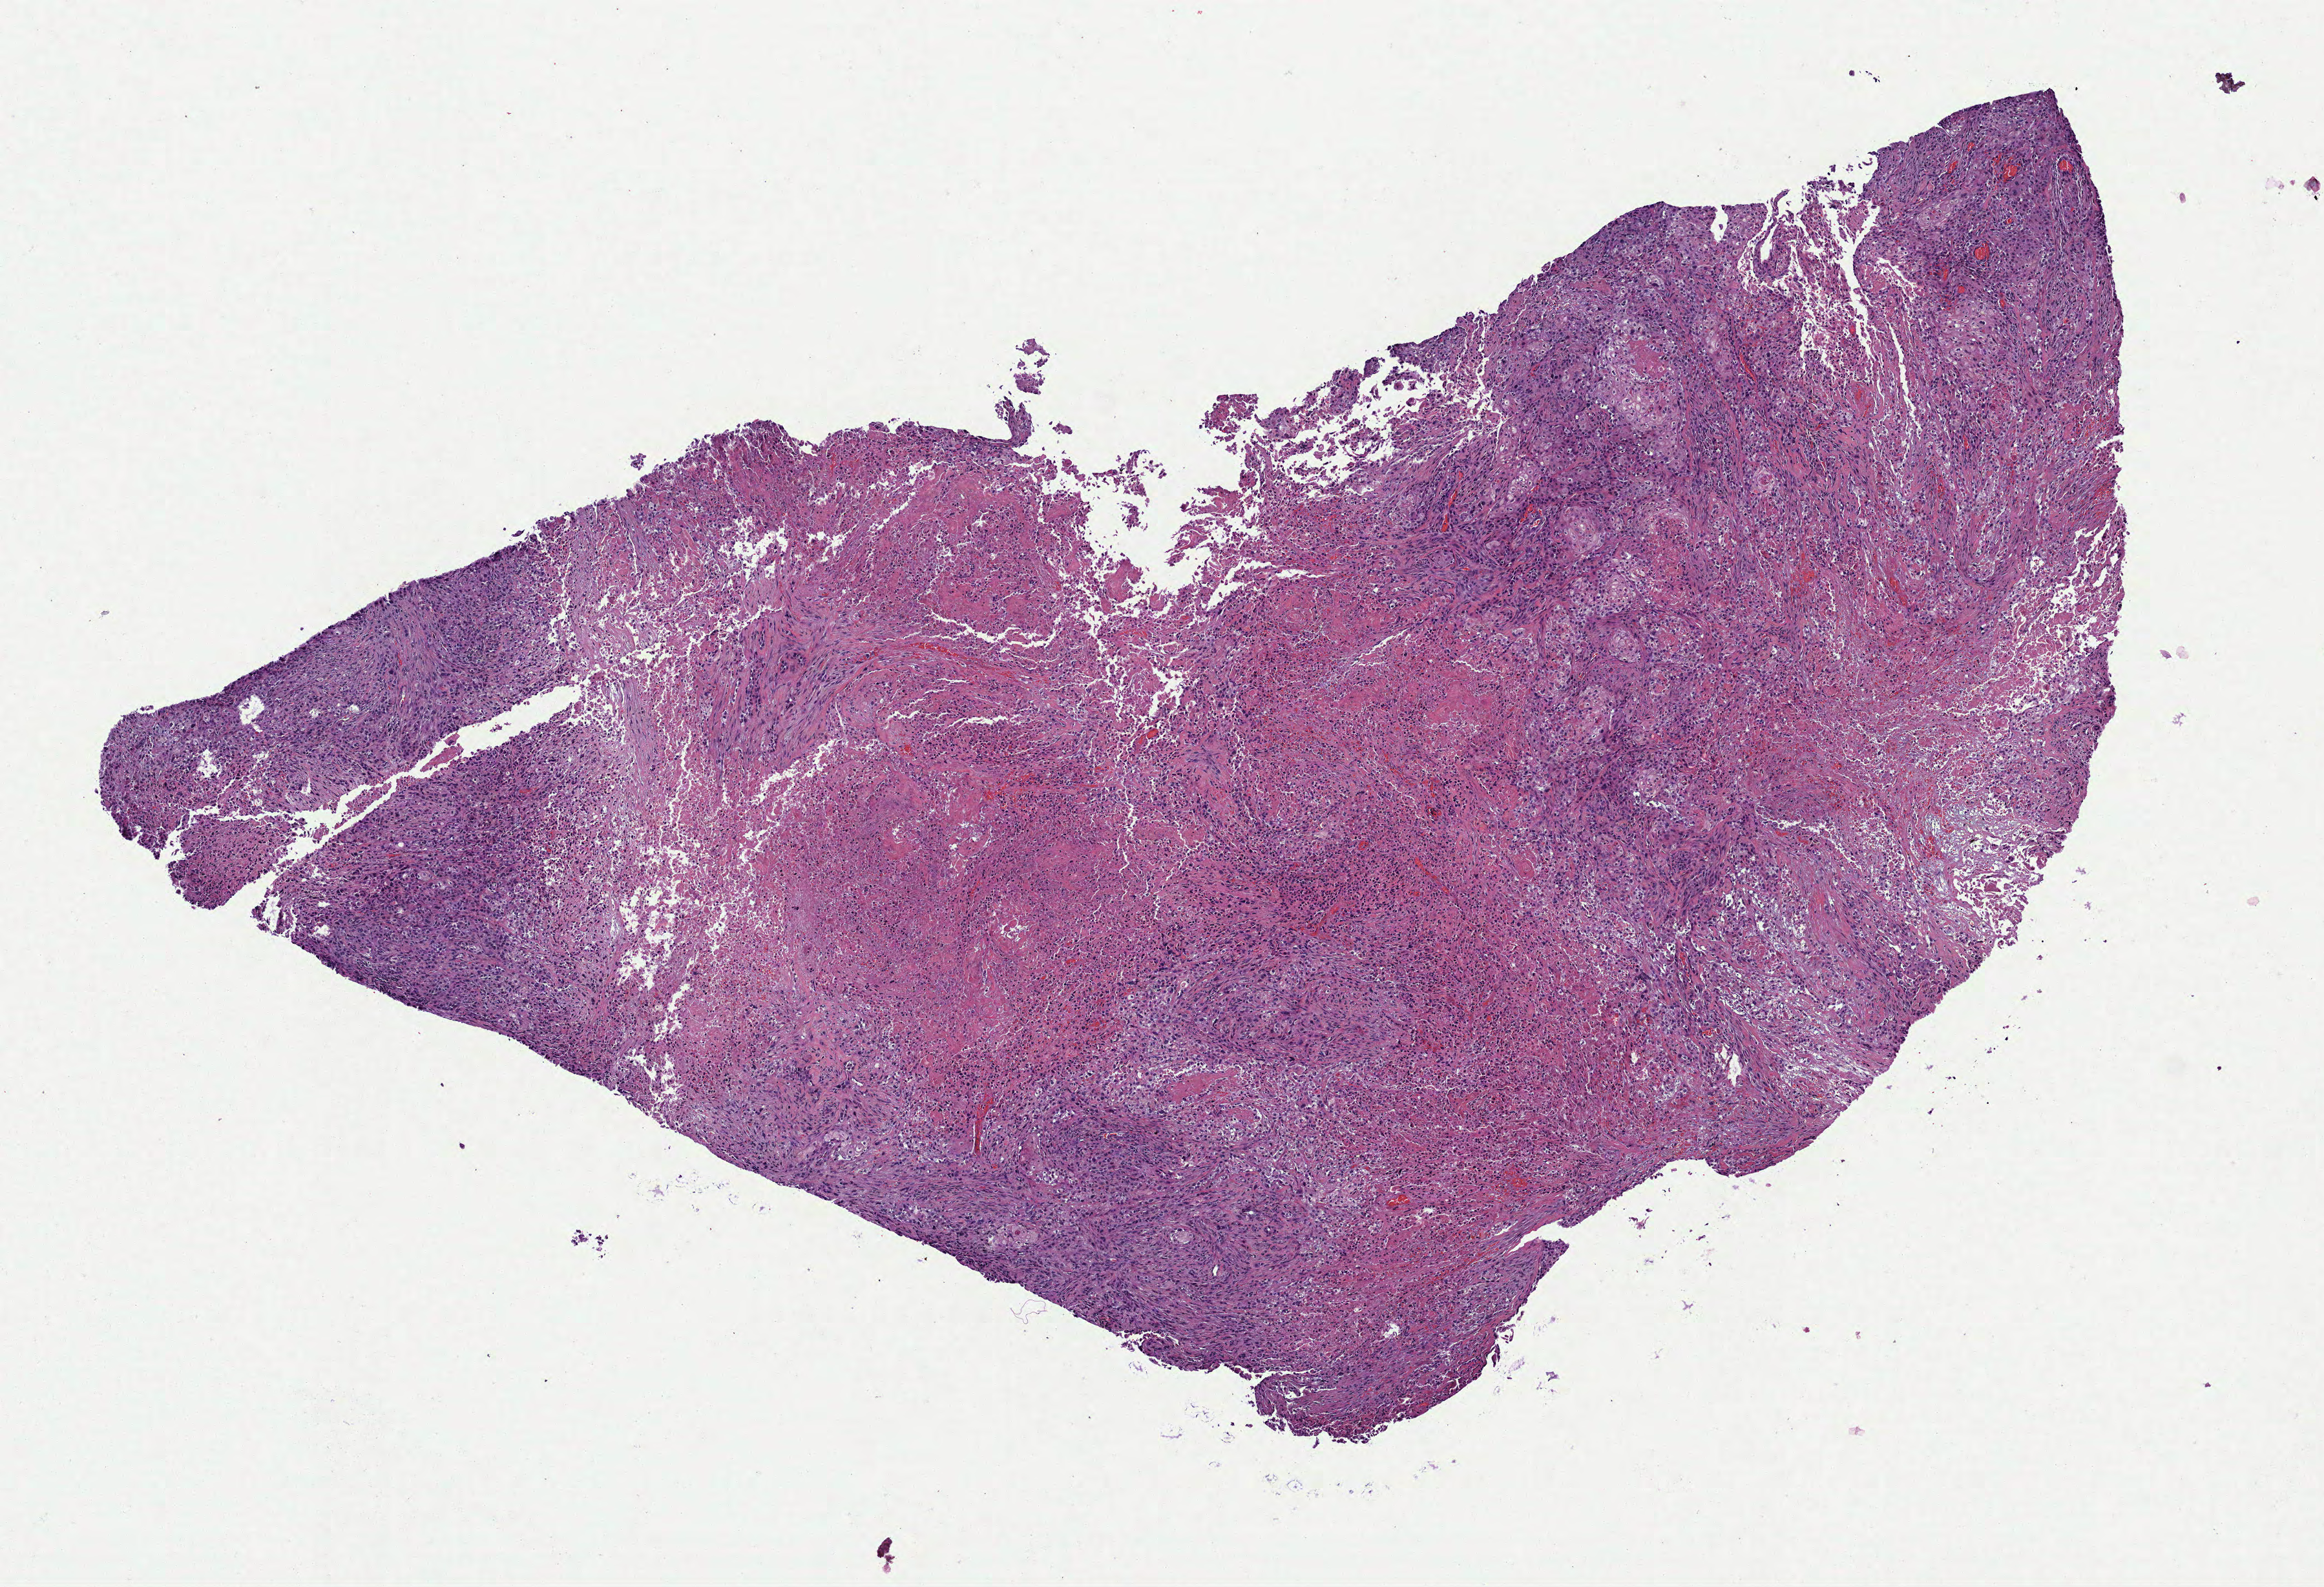
Hematoxylin and eosin (H&E) stained whole-slide image — a low-resolution overview of the entire scanned area, about 7.3 x 5.0 mm (acquisition: 40x scan). Formalin-fixed paraffin-embedded (FFPE) diagnostic section. Primary tumour sample from the head and neck. Male patient; age at initial diagnosis 74 years.
Diagnosis: Squamous cell carcinoma, keratinizing, NOS.